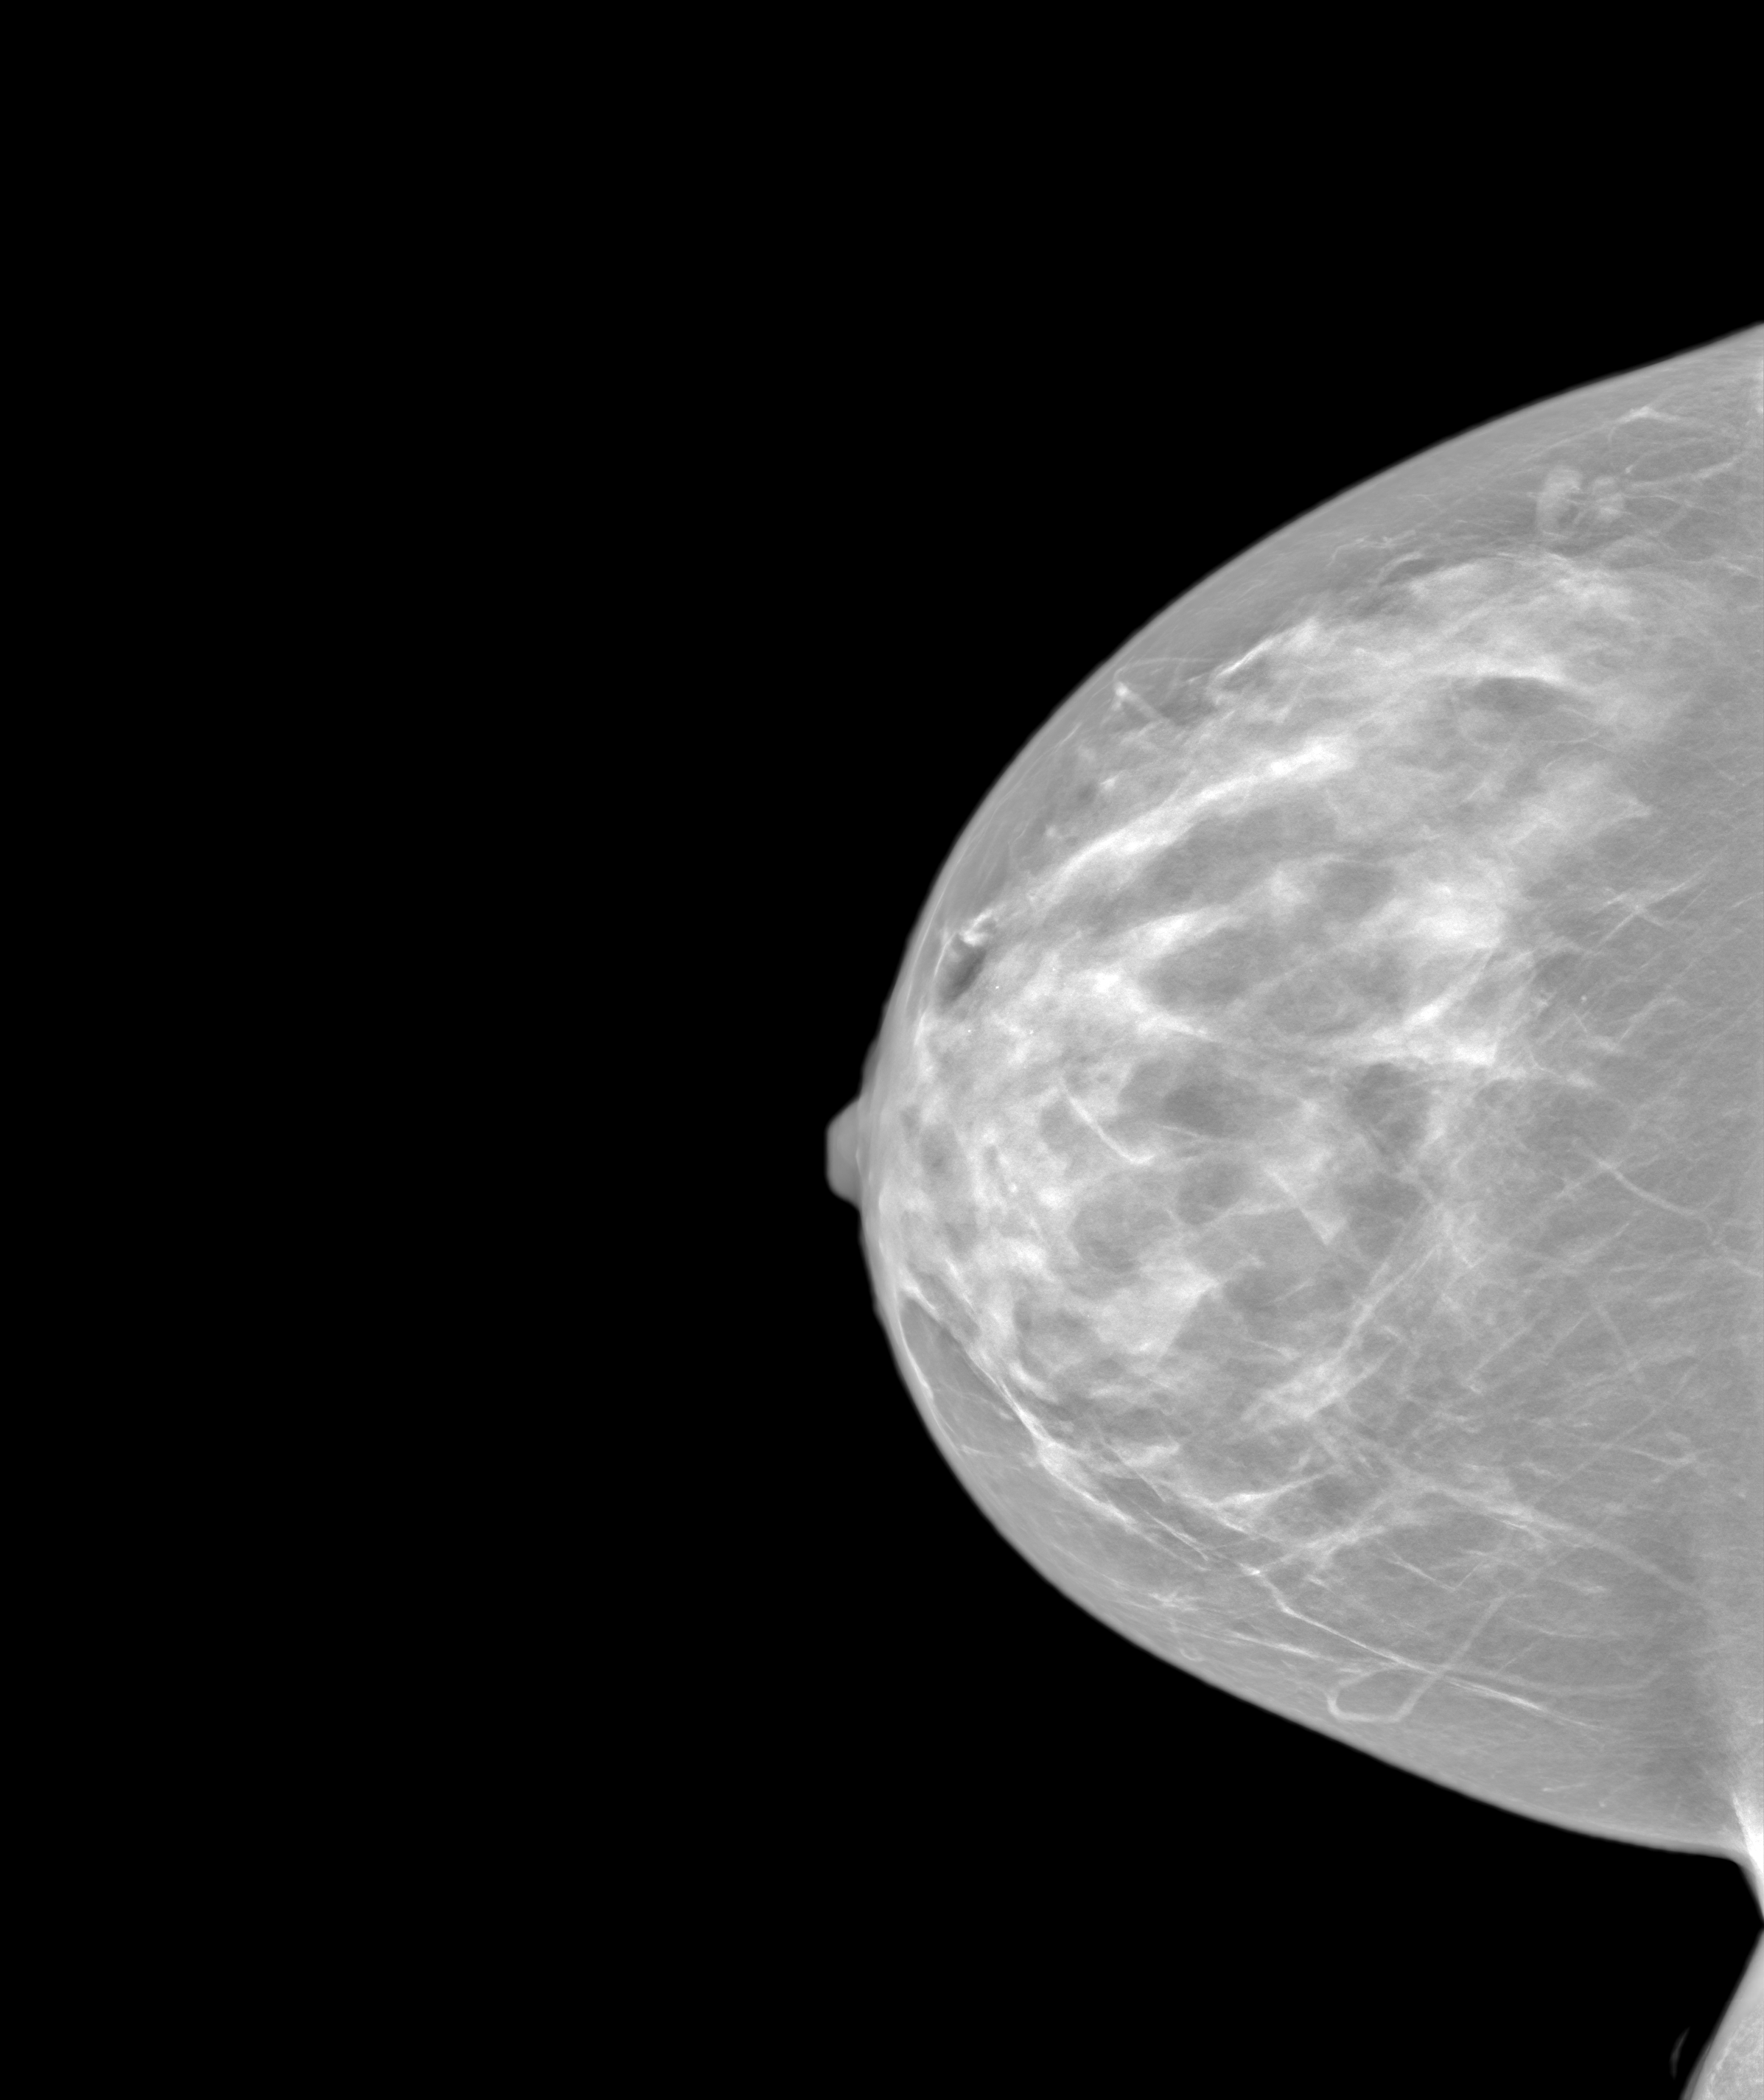
Screening examination, system: SenoIris_1SP2(440). Female patient, age 47 years.
Image type: synthesized 2-D view from tomosynthesis. Breast: right. Projection: CC view.